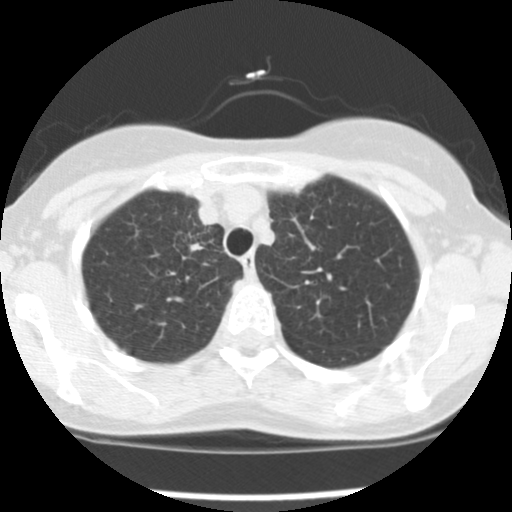
Low-dose screening chest CT, one axial slice; slice 123 of 157 in the series (ordered by position); 120 kVp; lung window (W 1500 / L -600 HU); 2.5 mm slice thickness; 512 × 512 image matrix, field of view 282 × 282 mm.
Annotated regions visible in this slice (outlined manually by an expert reader):
- lesion 1 (tumor, upper lobe of right lung): box from (x=190, y=243) to (x=204, y=252) px